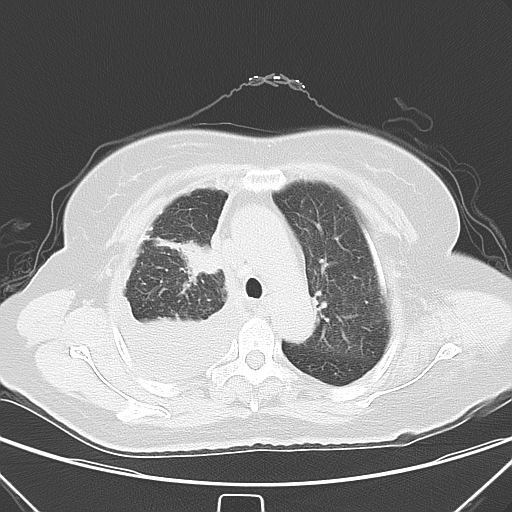
Chest CT, one axial slice. Slice 42 of 55 in the series (ordered by position). 120 kVp. Lung window (W 1500 / L -600 HU). 5 mm slice thickness. 512 × 512 image matrix, field of view 352 × 352 mm. Patient: female, 66 years. From the clinical record (not read from this slice): clinical TNM (as recorded): T2 N0 M1.
Annotated regions visible in this slice (bounding box drawn by a radiologist):
- lung tumour (recorded histology: adenocarcinoma): bounding box <154,228,219,280> (left, top, right, bottom; pixels)